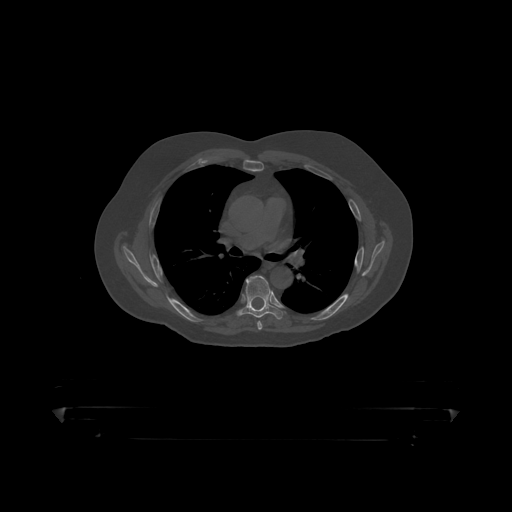
CT including the spine, one axial slice. Position 304 of 390 along the scan axis. Reconstruction kernel STANDARD. 120 kVp. Bone window (W 1800 / L 400 HU). 1.25 mm slice thickness. 512 × 512 image matrix, field of view 650 × 650 mm. Male patient, age 60 years. From the clinical record (not read from this slice): primary cancer: prostate.
Annotated regions visible in this slice (semi-automatically segmented with operator editing):
- T6 vertebra: bounding box <237,276,283,319> (left, top, right, bottom; pixels)